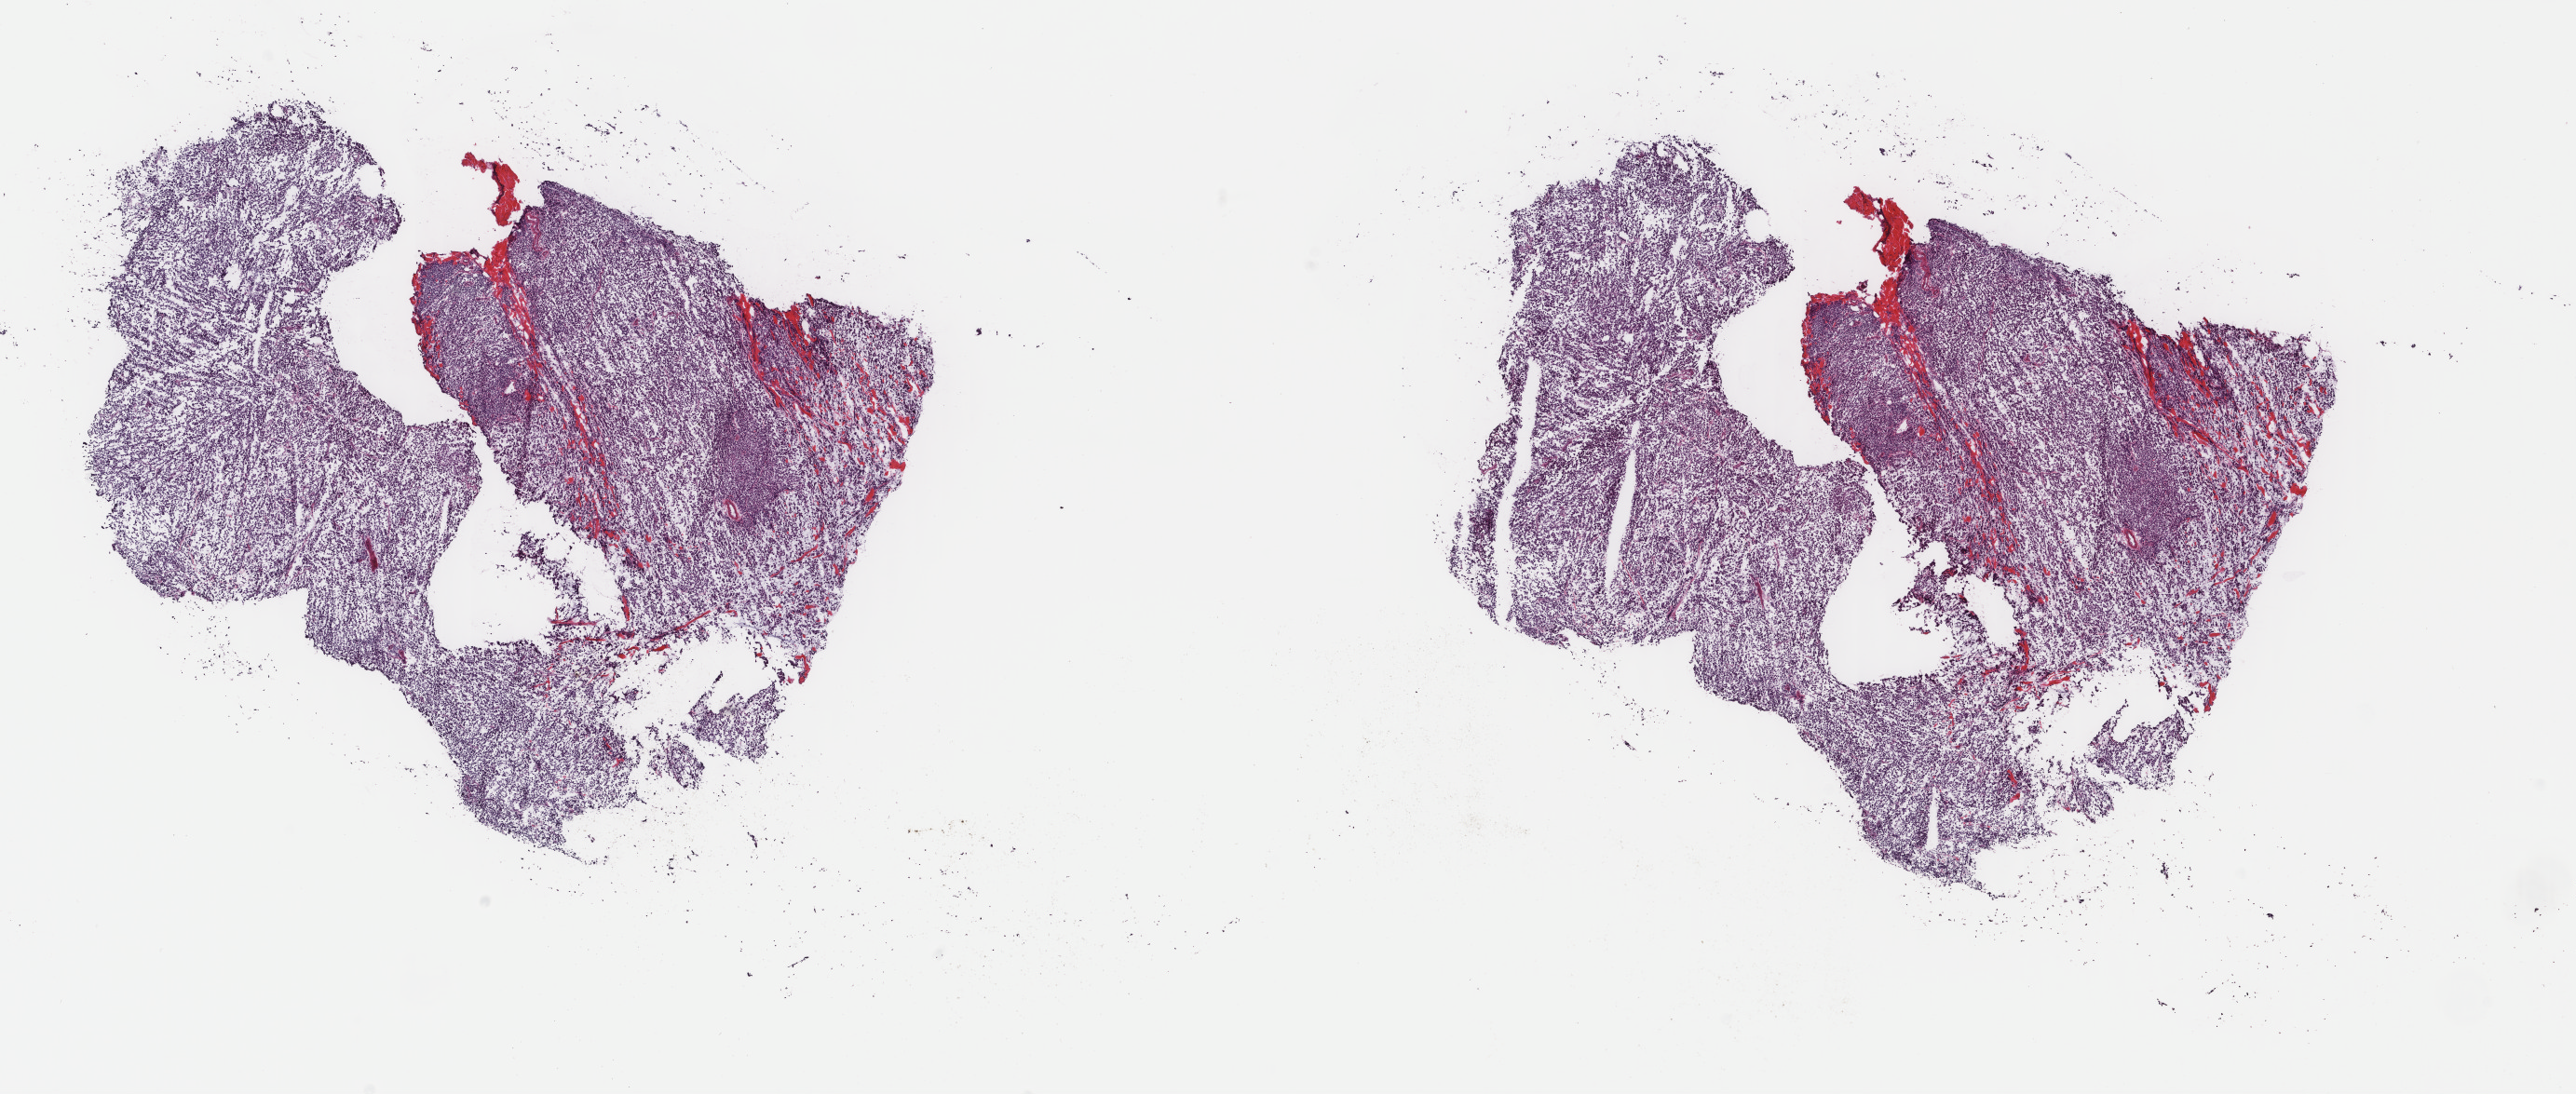
Whole-slide histology image, Hematoxylin and eosin (H&E) stained, low-resolution overview of the scanned area, about 22.0 x 9.3 mm (acquisition: 40x scan), frozen section from the top of the tissue portion, metastatic tumour sample. Female, age 74 years at initial diagnosis. Pathologist review of this section (percent, as recorded): tumour cells 85%, tumour nuclei 85%, normal cells 0%, stromal cells 15%, necrosis 0%. Infiltration values recorded for this section: lymphocyte infiltration 3%, monocyte infiltration 0%, neutrophil infiltration 0%.
* this section: metastatic tumour tissue
* patient diagnosis: Malignant melanoma, NOS